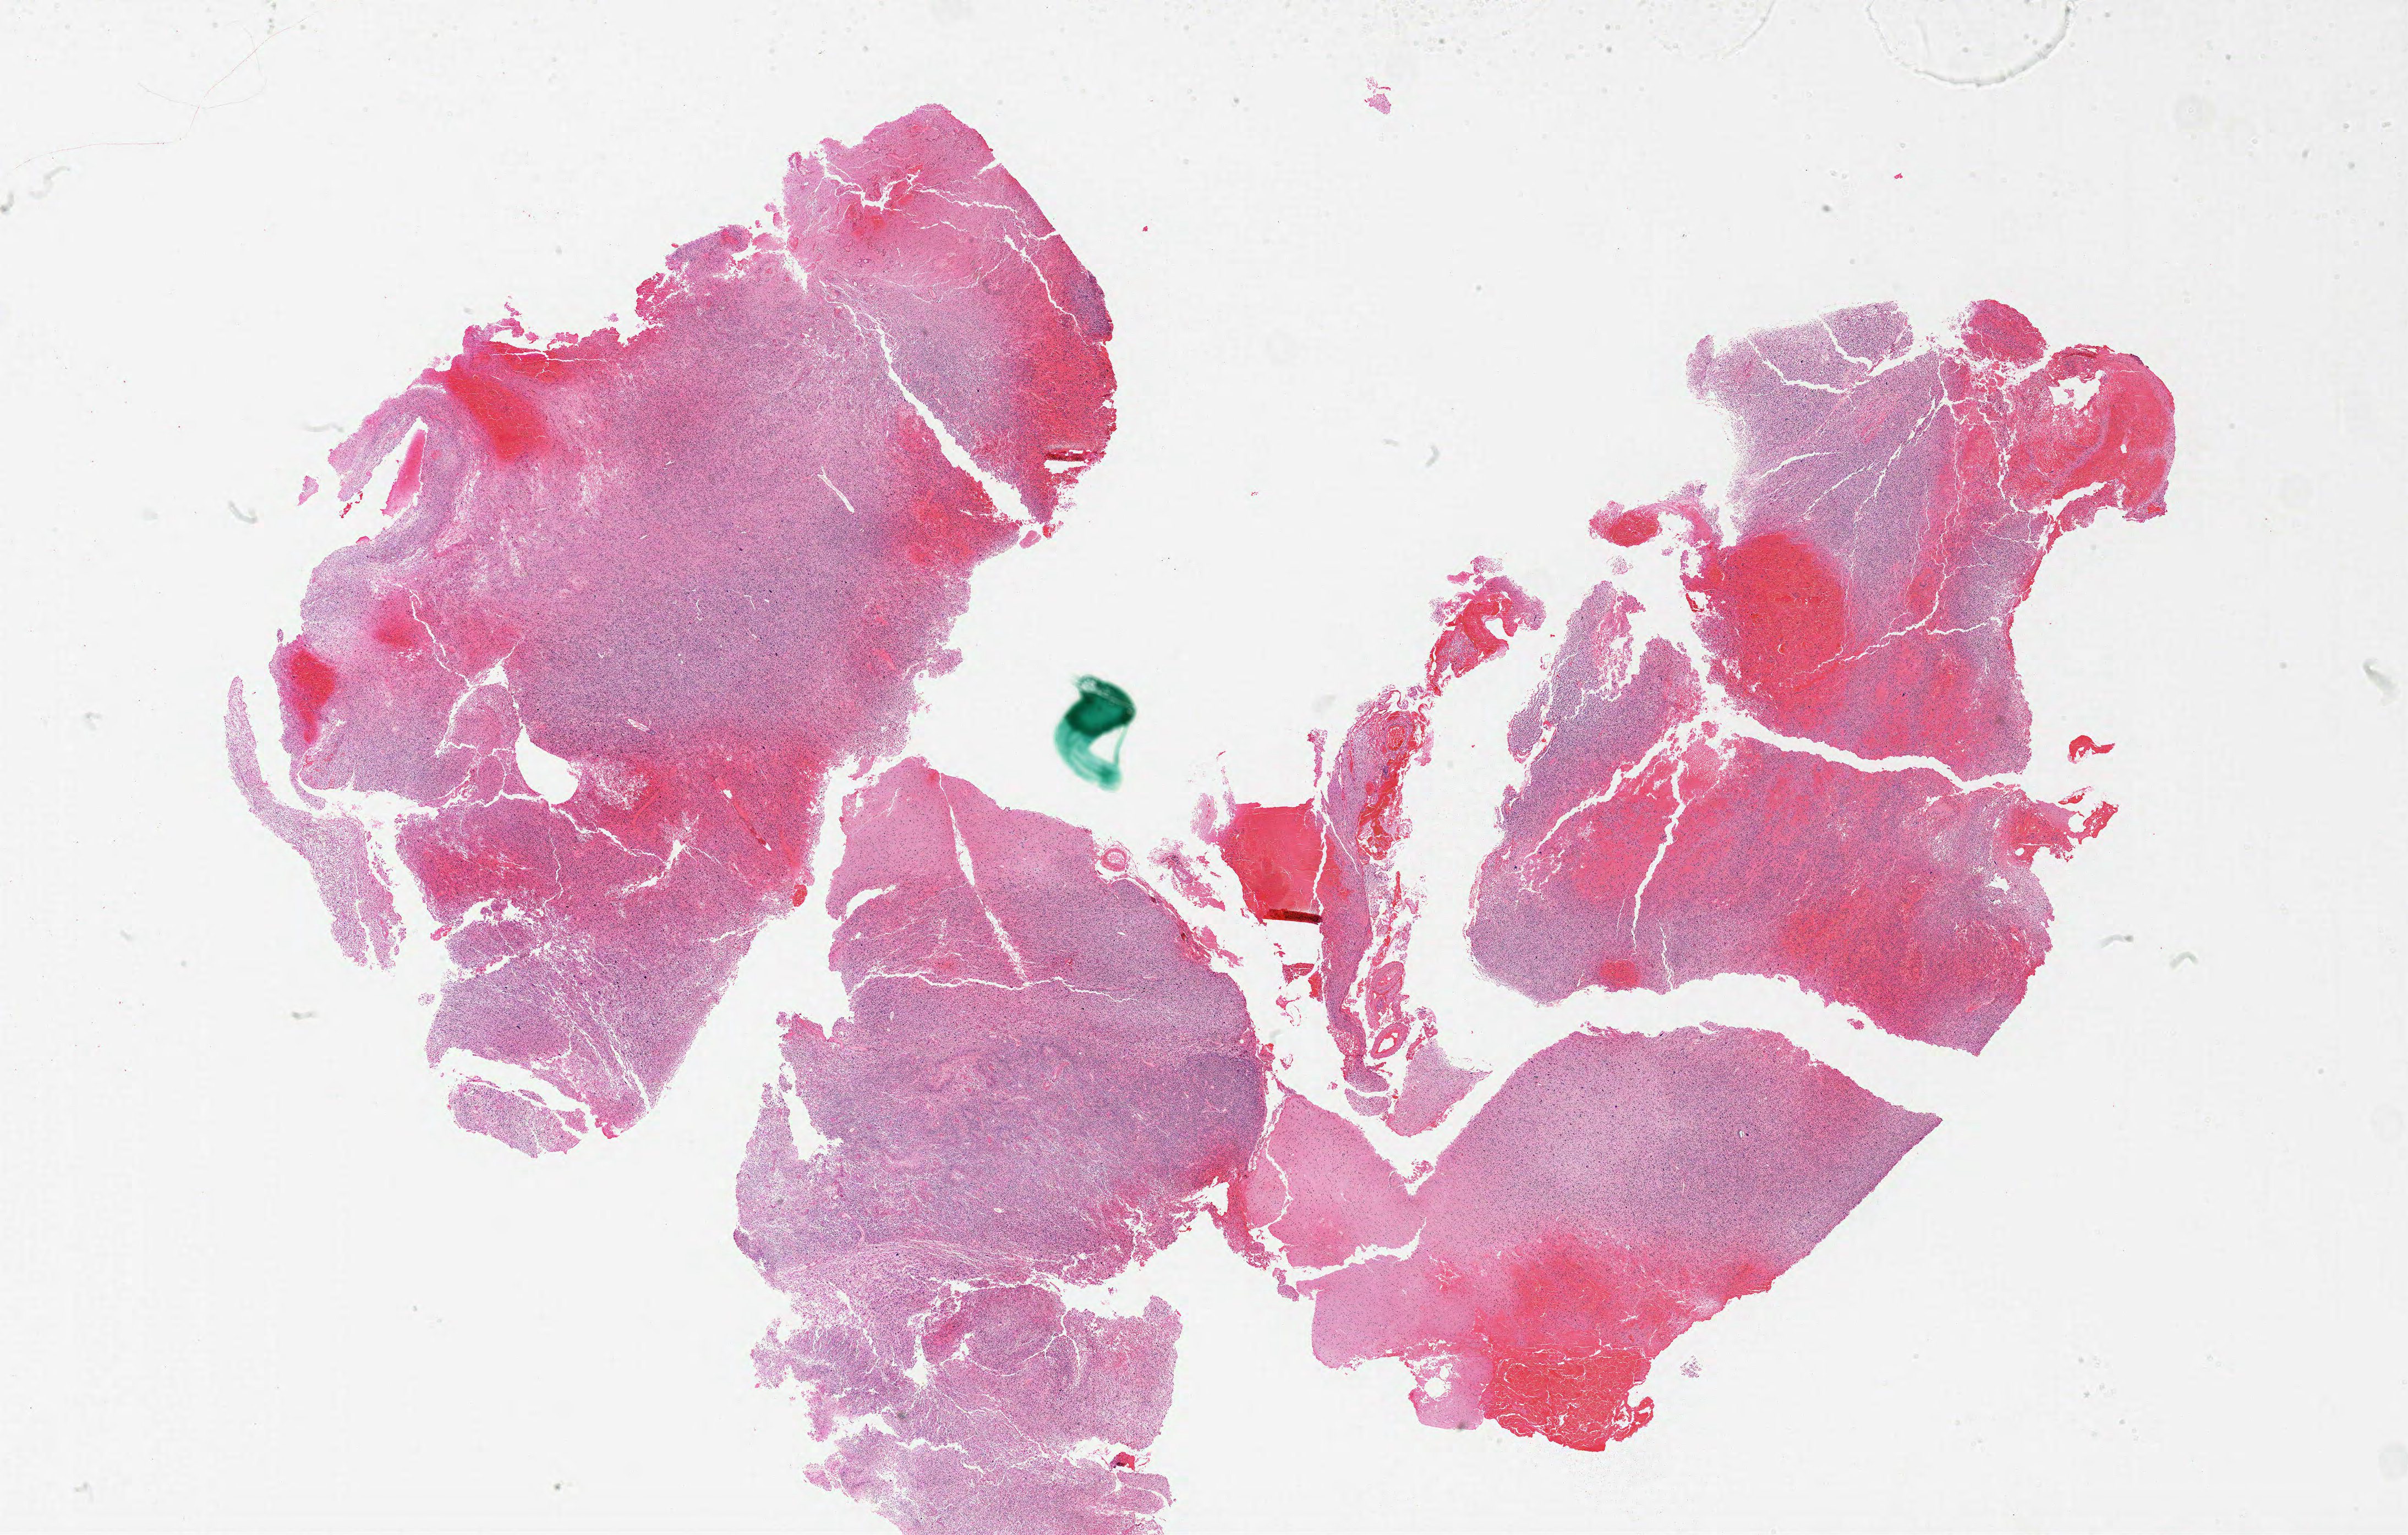
Whole-slide histology image, Hematoxylin and eosin (H&E) stained, whole scanned area (about 35.0 x 22.3 mm) shown as a low-resolution overview, FFPE section, sample: primary tumour, brain. Male patient; age at initial diagnosis 51 years.
Diagnosis: Glioblastoma.